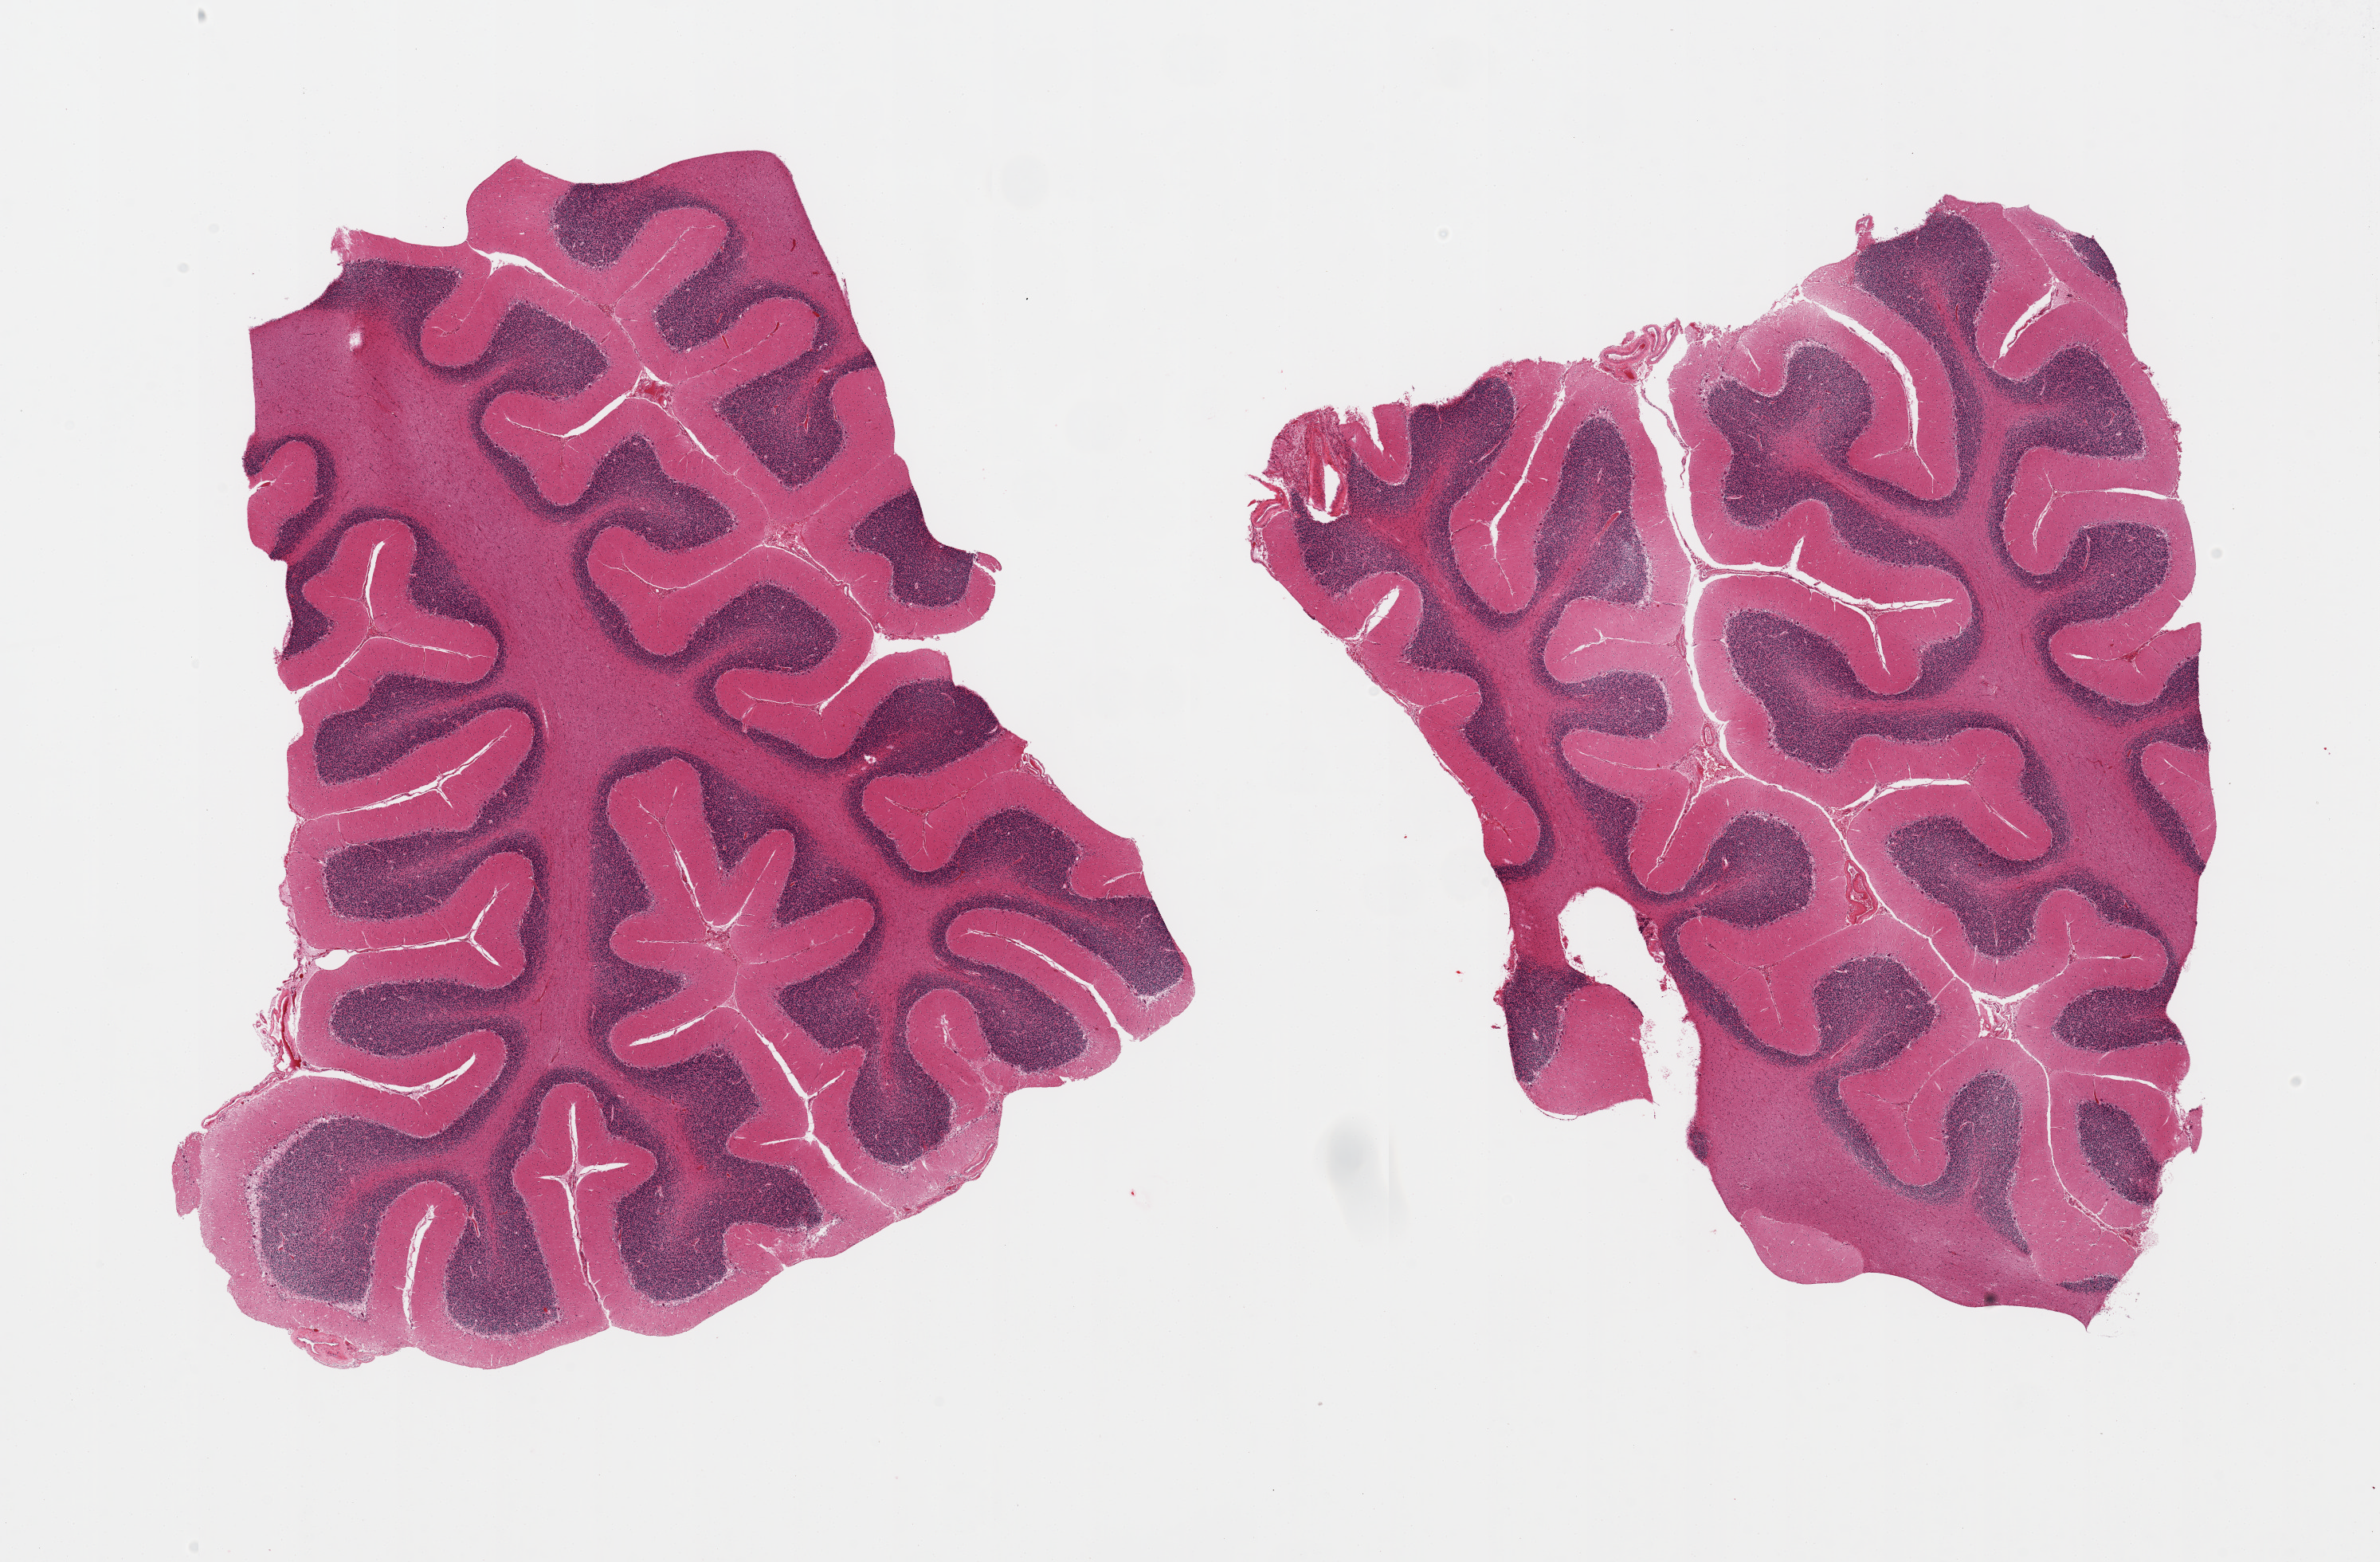
Whole-slide image, hematoxylin and eosin (H&E) stain — whole scanned area (about 23.6 x 15.5 mm) shown as a low-resolution overview, PAXgene-fixed, paraffin-embedded tissue, target tissue: cerebellum, tissue donor sample.
• reviewer comment on this tissue sample: 2 pieces, no abnormalities